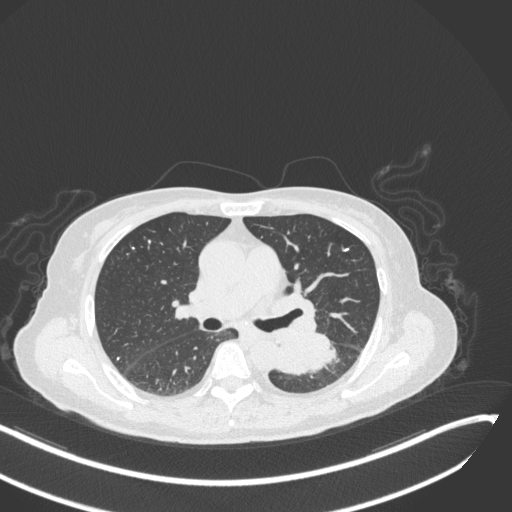
Chest CT, one axial slice; position 164 of 342 along the scan axis; reconstruction kernel B31f; 120 kVp; lung window (W 1500 / L -600 HU); 1 mm slice thickness; 512 × 512 image matrix. Female patient, age 64 years. Case-level facts recorded for this patient, not image findings: clinical TNM (as recorded): T3 N1 M1.
Structures marked on this image (rectangle marked by the reading radiologist):
- lung tumour (recorded histology: small cell carcinoma): bounding box <276,328,340,378> (left, top, right, bottom; pixels)